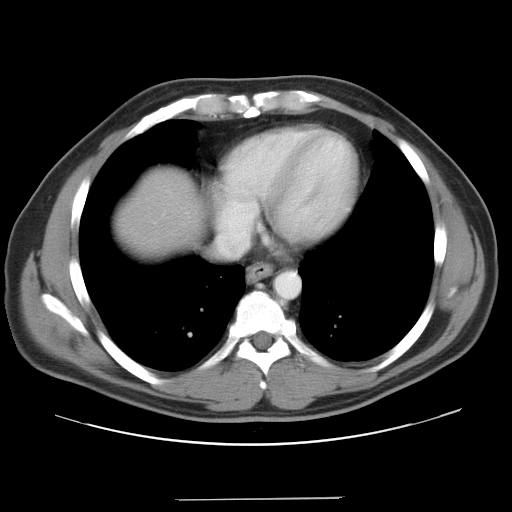
Contrast-enhanced abdominal CT, one axial slice. Position 36 of 37 along the scan axis. Reconstruction kernel STANDARD. 120 kVp. Intravenous contrast given. Soft-tissue window (W 400 / L 40 HU). 7.5 mm slice thickness. 512 × 512 image matrix, field of view 400 × 400 mm. Male patient, age 46 years. Case-level facts recorded for this patient, not image findings: diagnosis: colorectal cancer liver metastases, imaged before liver resection; multiple liver metastases: yes; largest metastasis: 1 cm; disease in both lobes: no.
Annotated regions visible in this slice (outlined manually by an expert reader):
- liver: box from (x=119, y=175) to (x=200, y=254) px
- planned liver remnant (the part of the liver to remain after resection): (x=120, y=175)–(x=200, y=254)